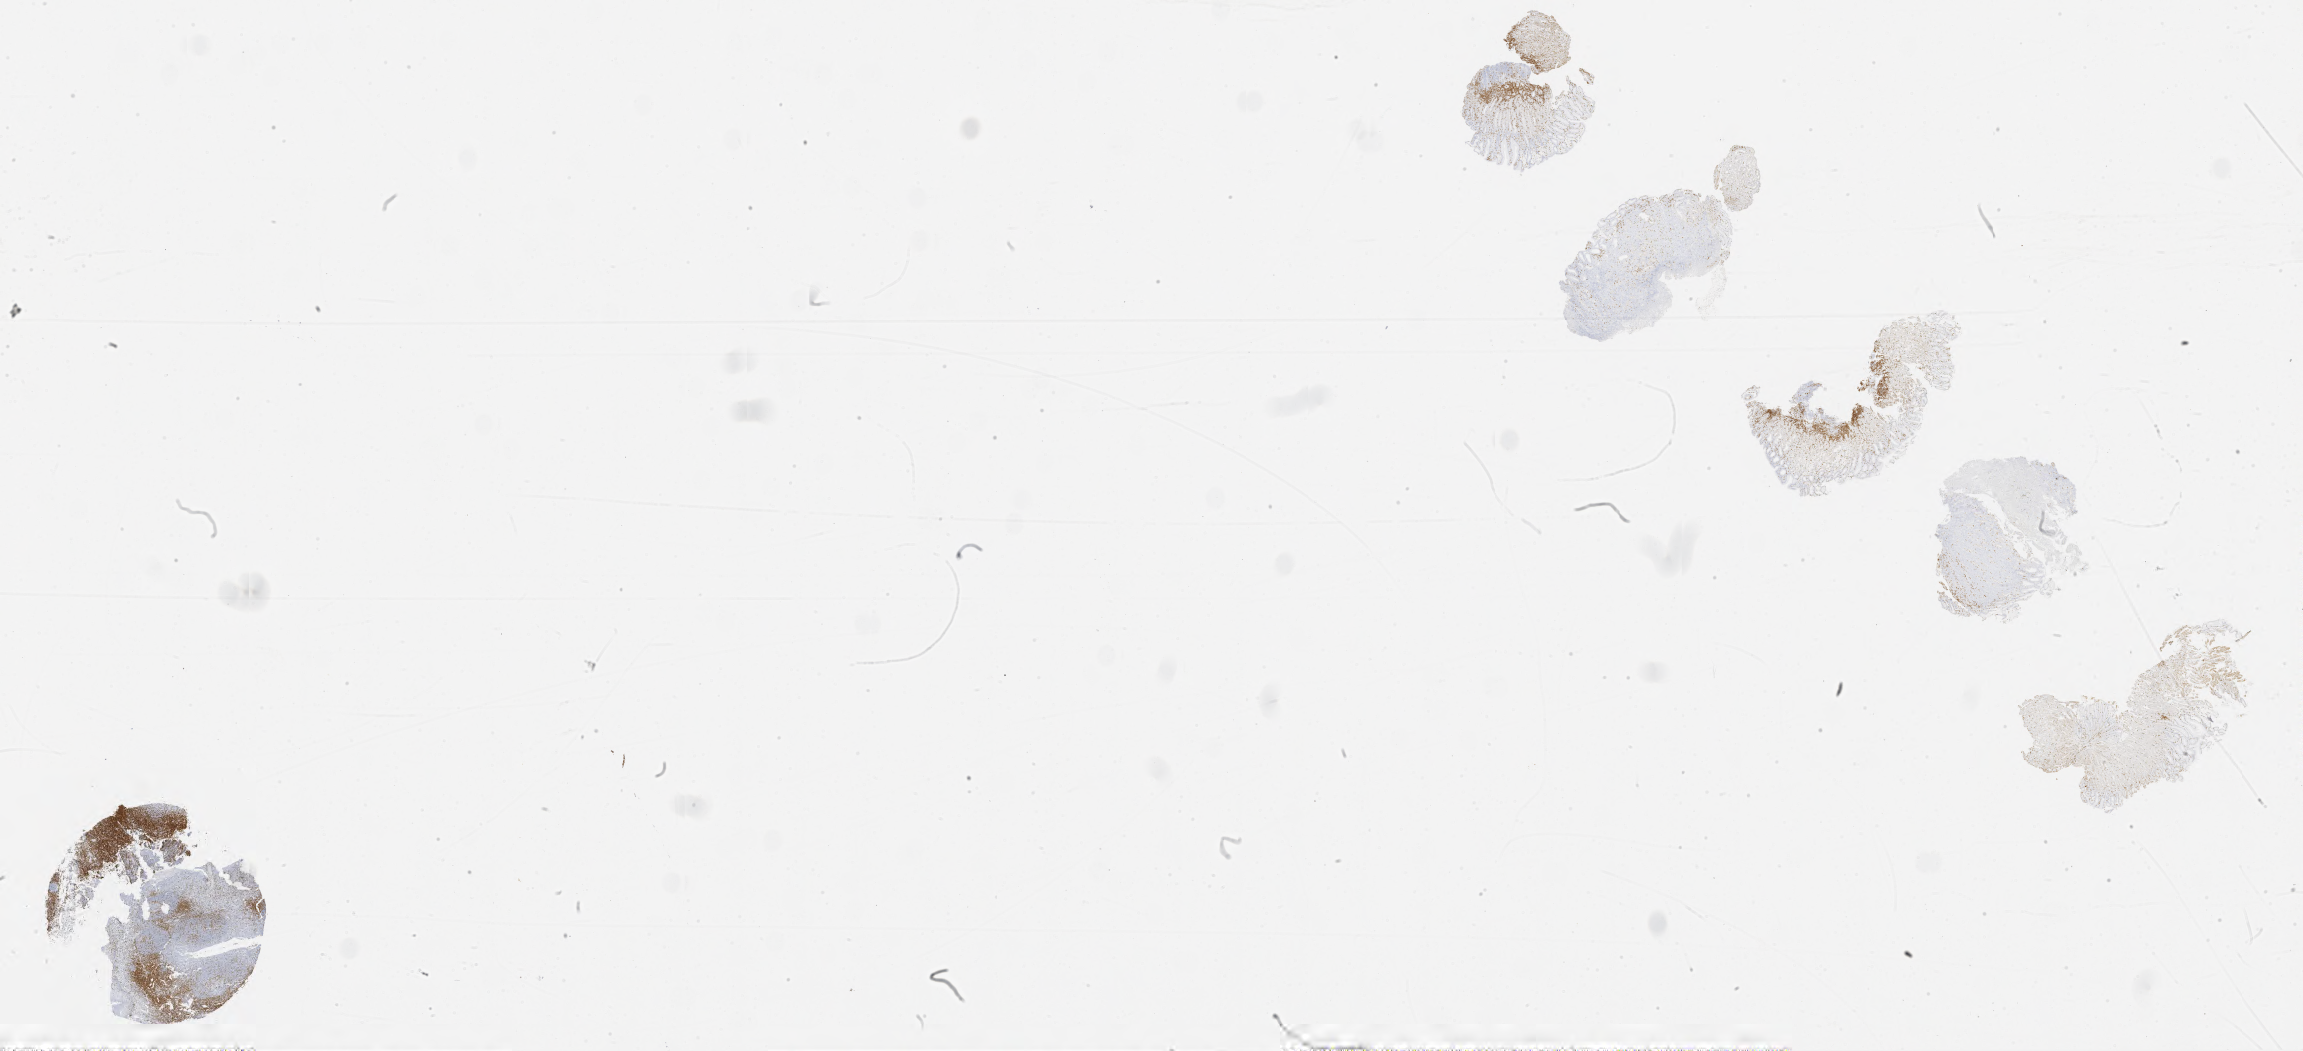
Immunohistochemistry (IHC) whole-slide image stained for CD3, whole scanned area (about 37.0 x 16.9 mm) shown as a low-resolution overview. Tumor tissue. Patient: male, 40 years old.
Histologic diagnosis: Burkitt lymphoma, NOS.